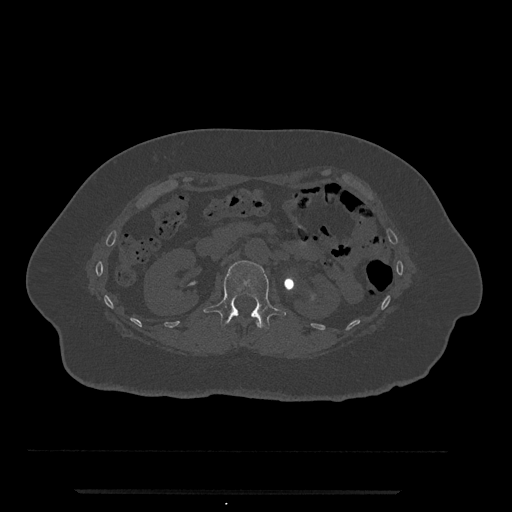
CT including the spine, one axial slice; slice 112 of 797 in the series (ordered by position); 120 kVp; bone window (W 1800 / L 400 HU); 512 × 512 image matrix. Female patient, age 51 years. Case-level facts recorded for this patient, not image findings: primary cancer: neuro; vertebrae with lytic lesions (as recorded): T8.
Structures marked on this image (semi-automatically segmented with operator editing):
- L1 vertebra: bounding box (x1, y1, x2, y2) in pixels: (203, 261, 286, 329)
- T12 vertebra: (256, 321, 261, 329)